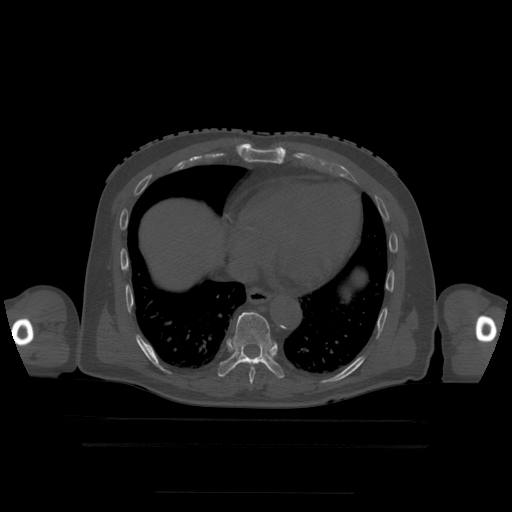
CT including the spine, one axial slice; slice 266 of 522 in the series (ordered by position); bone window (W 1800 / L 400 HU); 512 × 512 image matrix, field of view 436 × 436 mm. Patient age 68 years. From the clinical record (not read from this slice): primary cancer: urothelial.
Structures marked on this image (semi-automatically segmented with operator editing):
- T7 vertebra: box from (x=250, y=382) to (x=253, y=386) px
- T8 vertebra: (x=250, y=367)–(x=256, y=382)
- T9 vertebra: (x=218, y=312)–(x=285, y=379)